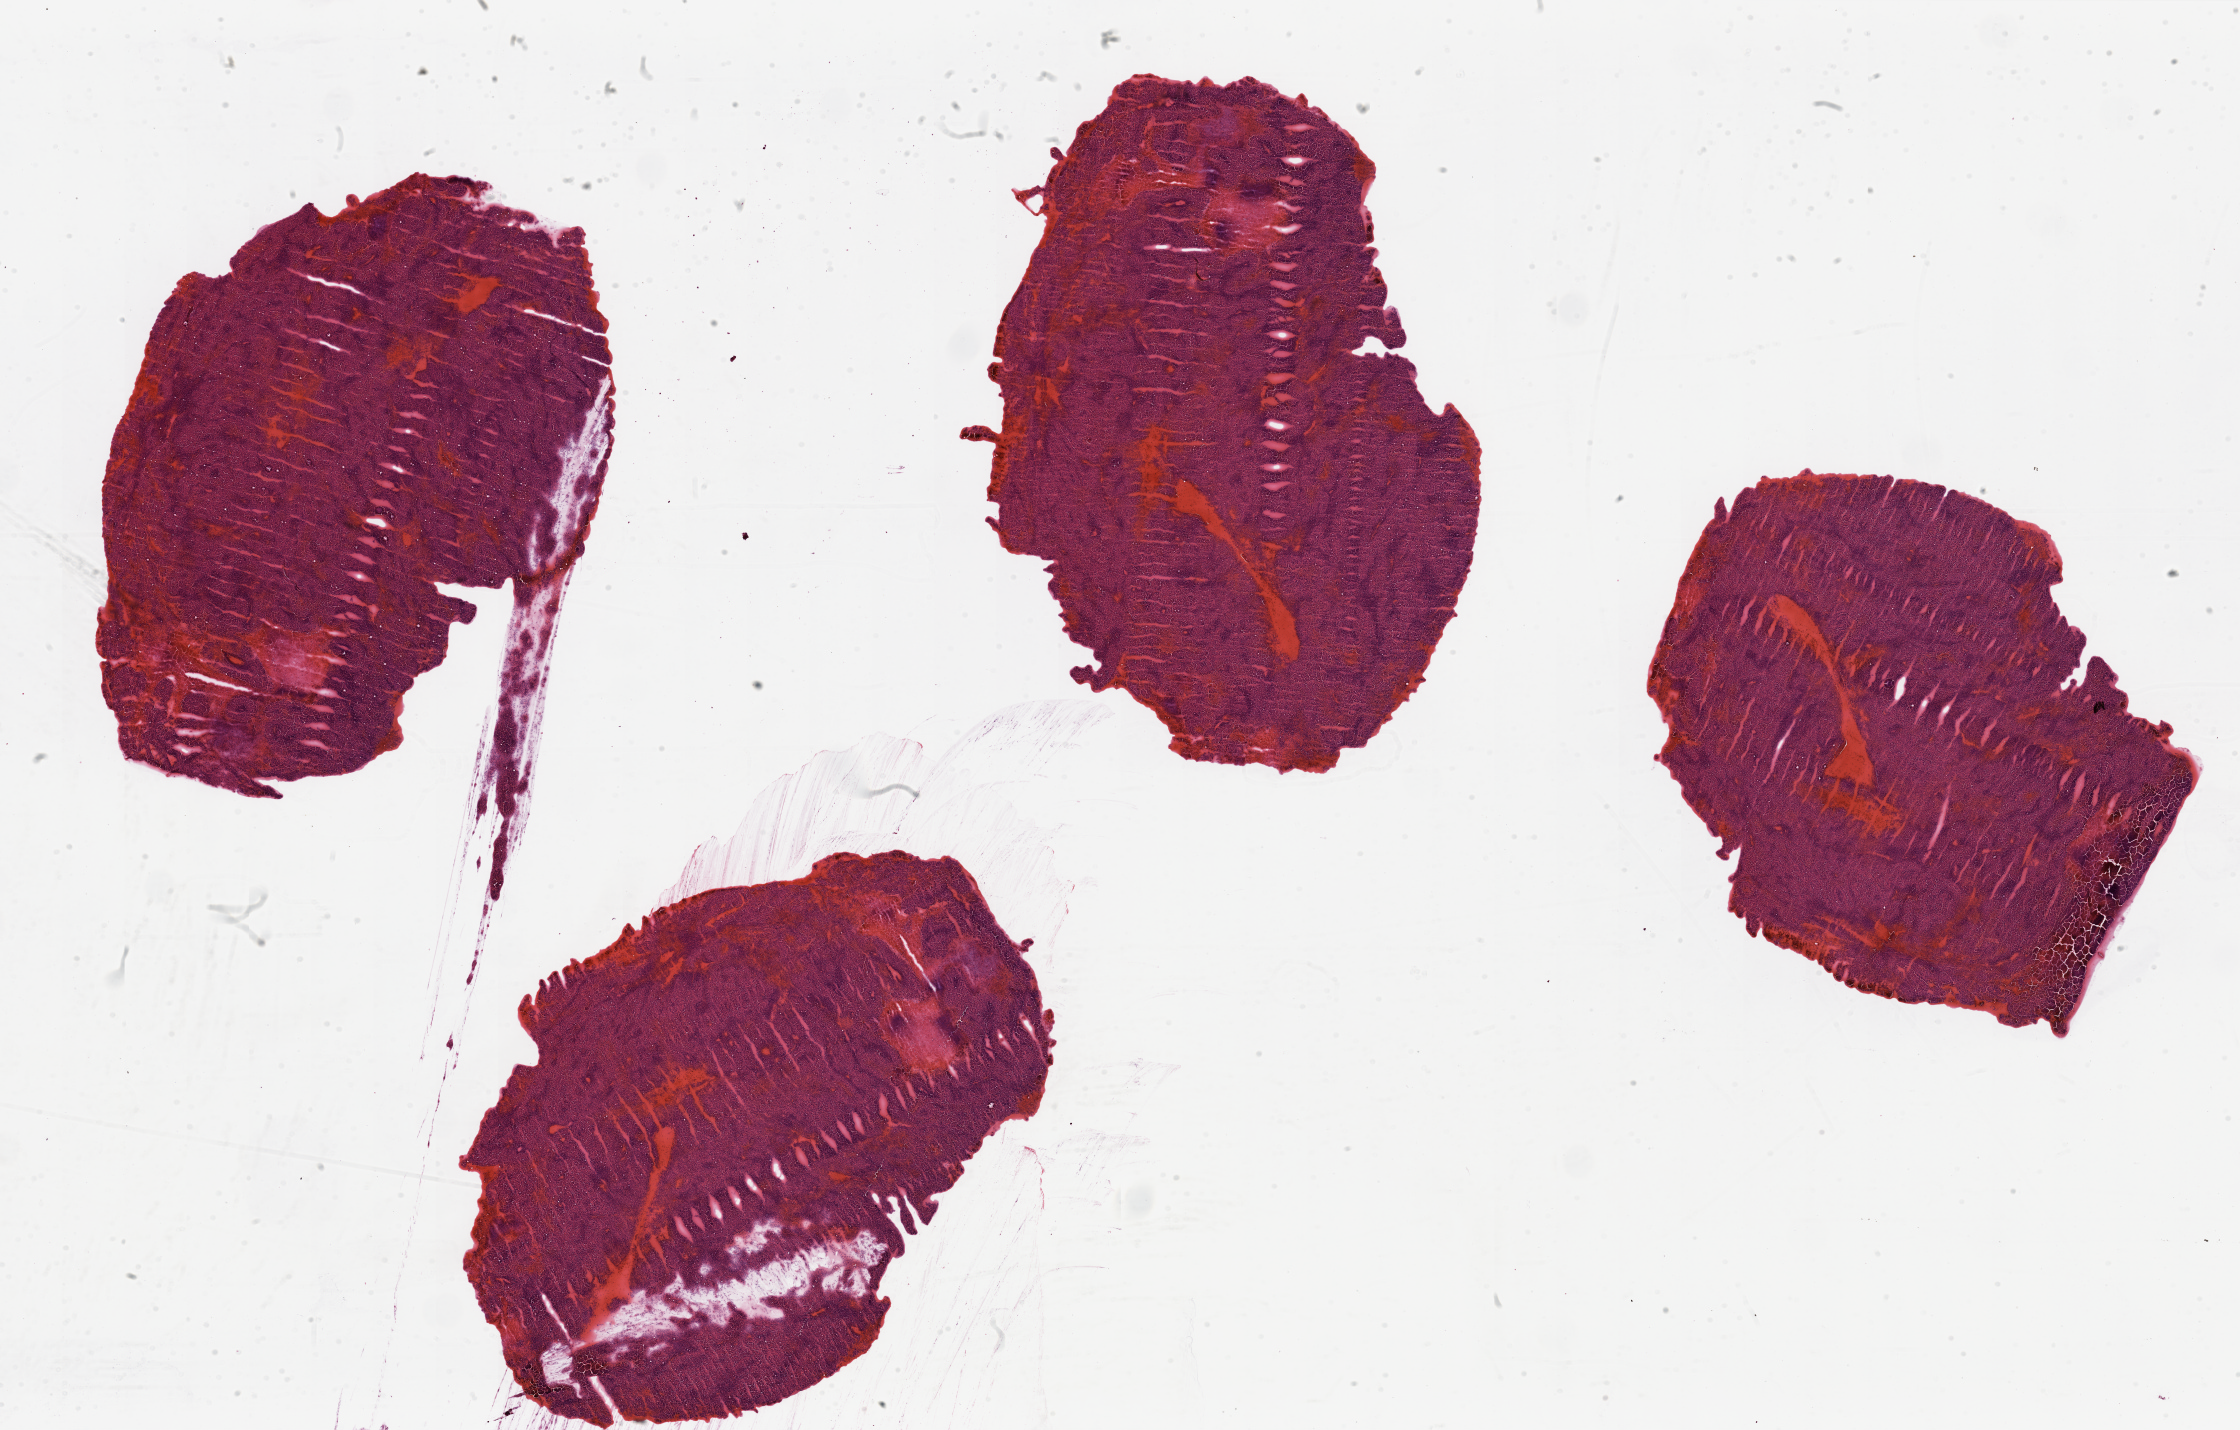
H&E whole-slide image, whole scanned area (about 35.4 x 22.6 mm, slide scanned at 20x) shown as a low-resolution overview. Tumour tissue sample, sampled site: kidney. Male, 68 y/o. Histologic grade: G3 (poorly differentiated). Composition of this section per pathologist review: tumour nuclei 90%, necrosis 15%.
Primary tumour site (as recorded): lower pole. AJCC pathologic stage: I. Diagnosis: Renal cell carcinoma, NOS.